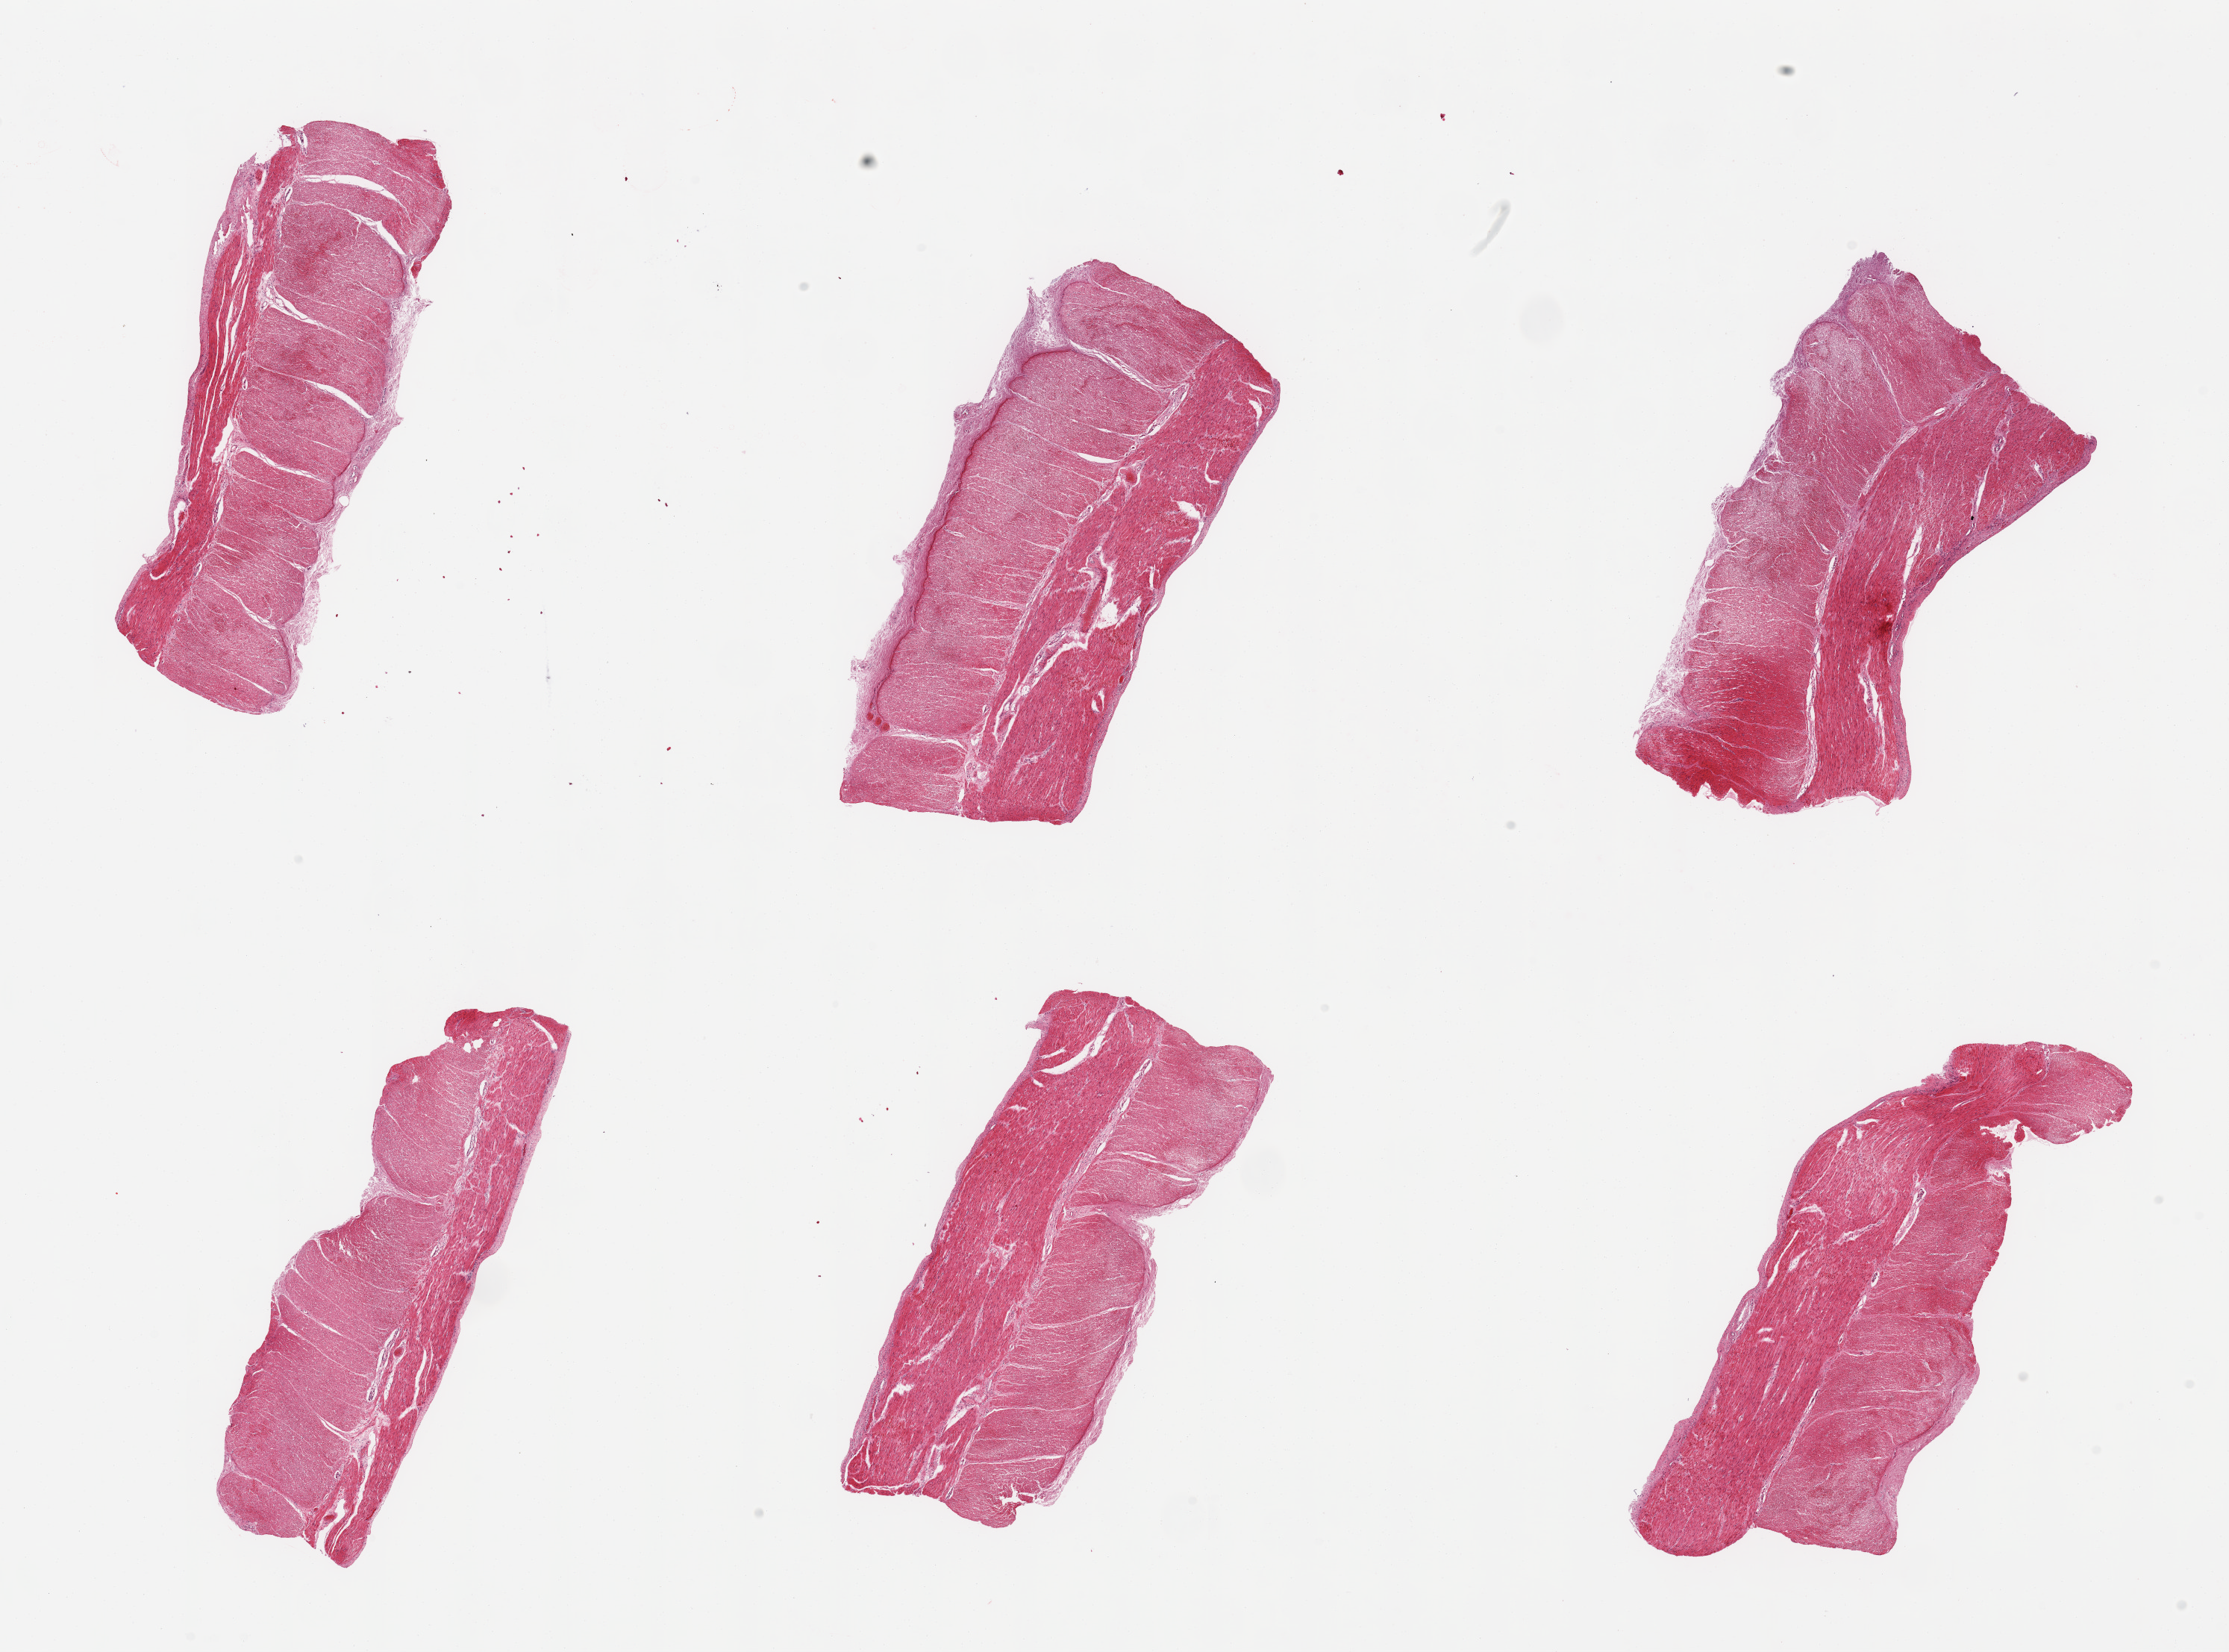
Digitized H&E-stained section — a low-resolution overview of the entire scanned area, about 23.6 x 17.5 mm (slide scanned at 20x). PAXgene-fixed, paraffin-embedded tissue. Section of sigmoid colon (target tissue). Tissue donor sample. Donor: female.
* pathologist's review note for this sample: 6 pieces, confirmed target muscularis